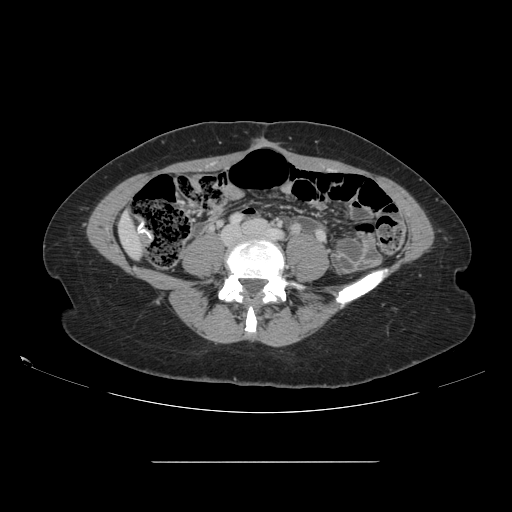
Contrast-enhanced abdominal CT, one axial slice. Slice 10 of 151 in the series (ordered by position). 120 kVp. Soft-tissue window (W 400 / L 40 HU). 2.5 mm slice thickness. 512 × 512 image matrix. Female patient, age 46 years. From the clinical record (not read from this slice): diagnosis: colorectal cancer liver metastases, imaged before liver resection; multiple liver metastases: yes; largest metastasis: 3 cm; chemotherapy before resection: no.
Annotated regions visible in this slice (expert manual segmentation):
- liver: box from (x=120, y=217) to (x=143, y=257) px
- planned liver remnant (the part of the liver to remain after resection): (x=120, y=217)–(x=143, y=257)